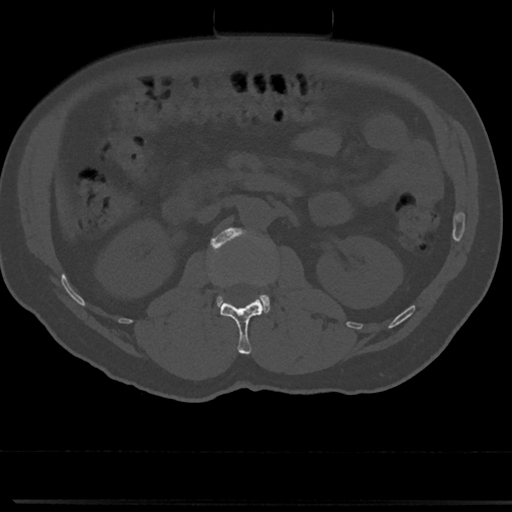
CT including the spine, one axial slice; slice 51 of 817 in the series (ordered by position); bone window (W 1800 / L 400 HU); 0.5 mm slice thickness; 512 × 512 image matrix, field of view 355 × 355 mm. Male patient, age 61 years. From the clinical record (not read from this slice): primary cancer: prostate.
Outlined on this slice (semi-automatic segmentation, software-assisted and operator-edited):
- L1 vertebra: box from (x=220, y=299) to (x=264, y=355) px
- L2 vertebra: (x=210, y=227)–(x=270, y=313)